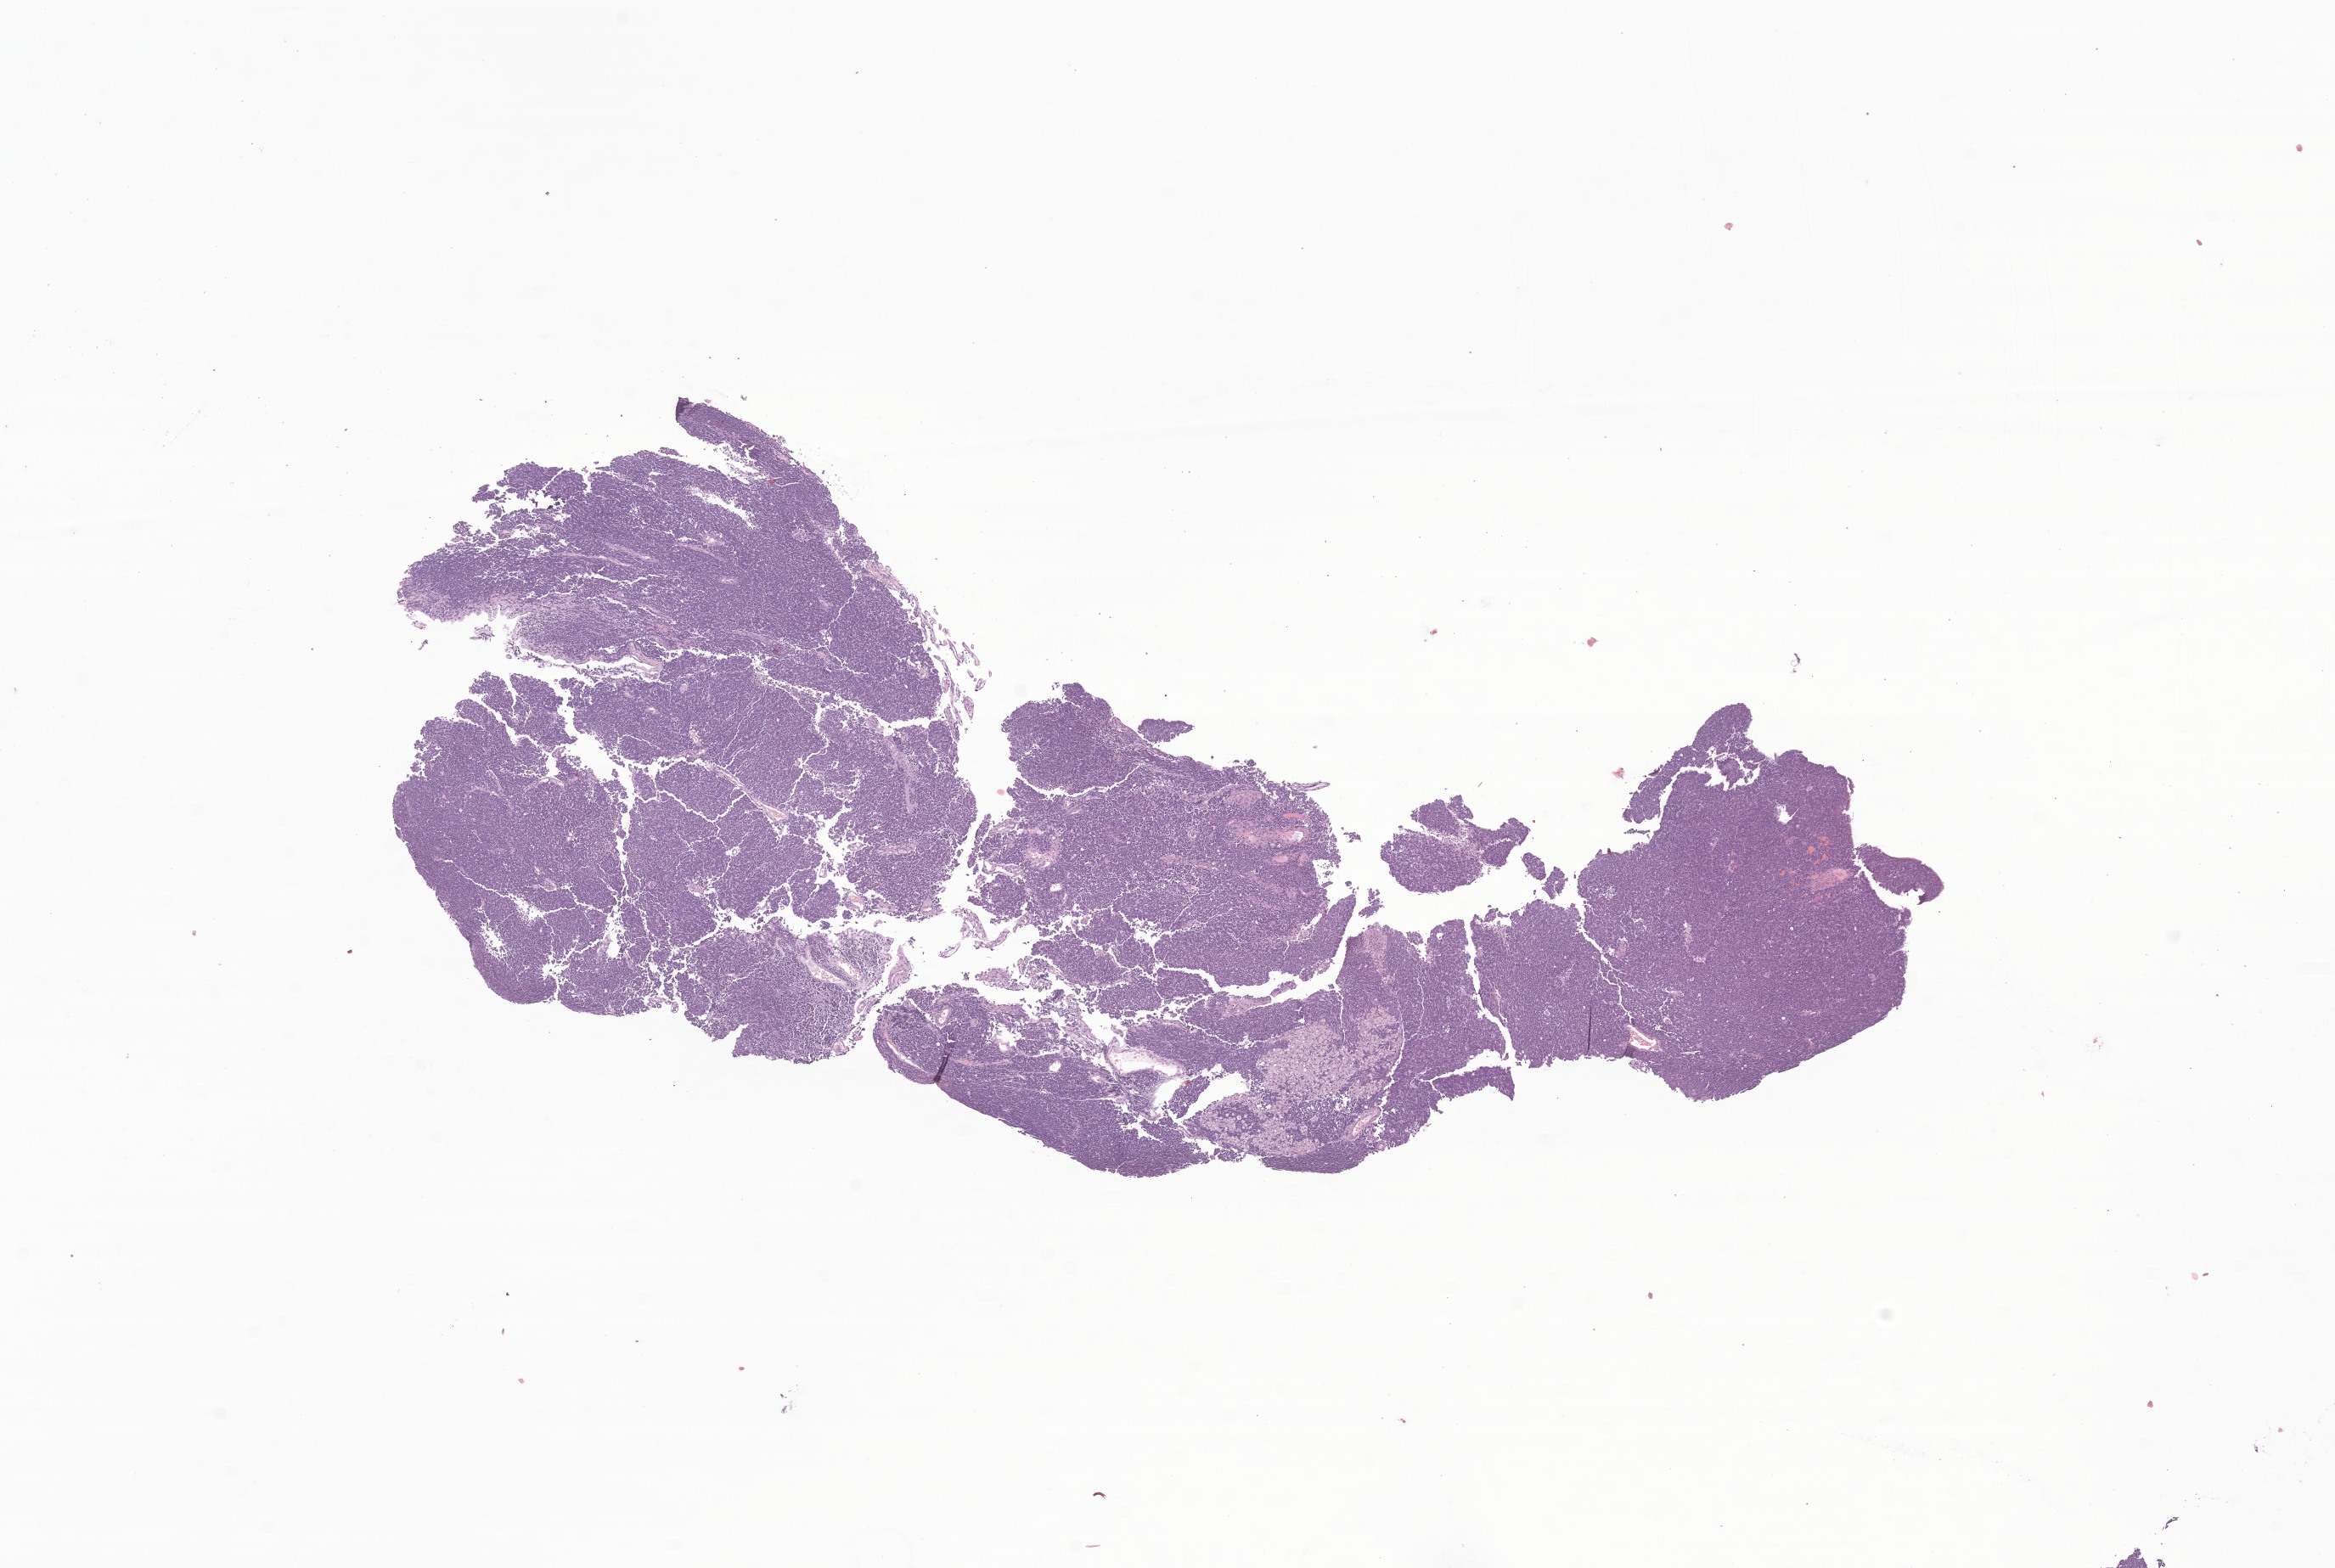
Hematoxylin and eosin (H&E) whole-slide image of tumor tissue from the pineal gland, low-resolution overview of the scanned area, about 11.6 x 7.8 mm. Formalin-fixed, paraffin-embedded (FFPE) tissue. Patient female; age 54 months (4 years 6 months).
Diagnosis (ICD-O-3 morphology term): Pineoblastoma.